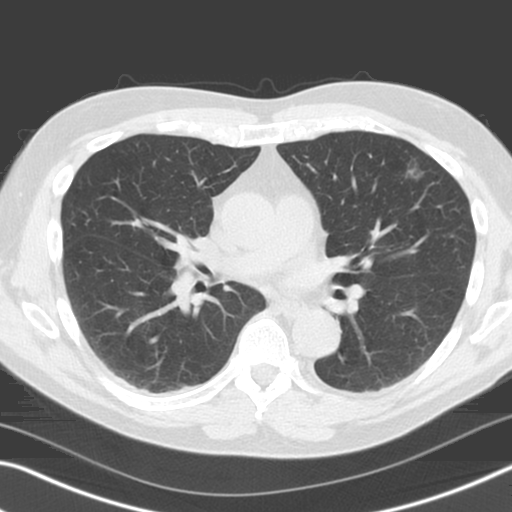
Low-dose screening chest CT, one axial slice; slice 82 of 165 in the series (ordered by position); 120 kVp; lung window (W 1500 / L -600 HU); 512 × 512 image matrix.
Structures marked on this image (outlined manually by an expert reader):
- lesion 1 (tumor, upper lobe of left lung): bounding box [x1, y1, x2, y2] px = [405, 165, 425, 180]